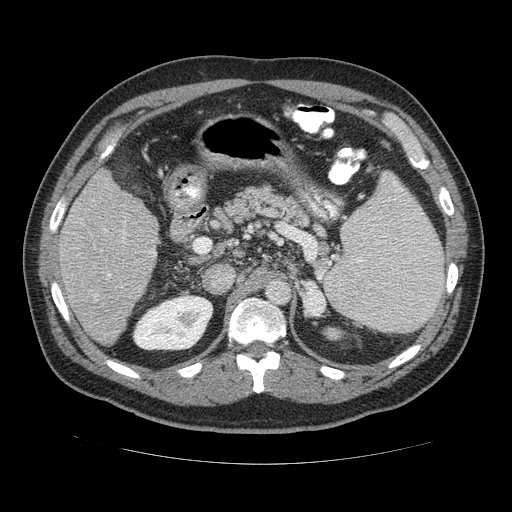
Contrast-enhanced abdominal CT (liver protocol), one axial slice. Slice 72 of 113 in the series (ordered by position). 120 kVp. Soft-tissue window (W 400 / L 40 HU). 2.5 mm slice thickness. 512 × 512 image matrix, field of view 400 × 400 mm. From the clinical record (not read from this slice): diagnosis: hepatocellular carcinoma (patient treated with transarterial chemoembolisation; whether this scan precedes or follows treatment is not stated here); TNM stage (as recorded): Stage-II; Child-Pugh class: B; tumour differentiation: moderately differentiated; tumour nodularity: multinodular.
Outlined on this slice (semi-automatically segmented with operator editing):
- liver parenchyma outside the tumour (the mass and vessels are separate outlines, so this box may not span the whole liver): bounding box <51,166,160,346> (left, top, right, bottom; pixels)
- liver vessels: <95,230,148,298>